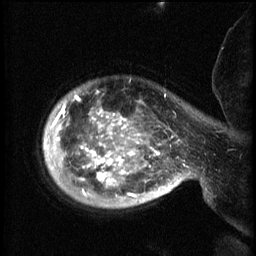
Breast MRI (dynamic contrast-enhanced), one sagittal slice. Position 51 of 60 along the scan axis. 3 images stored at this slice position (order not interpretable as contrast timing). 1.5 T. TE 4.2 ms, TR 8.2 ms. 2.3 mm slice thickness. 256 × 256 image matrix. Patient: female, 50 years.
Outlined on this slice (semi-automatically segmented with operator editing):
- analysis volume of interest (the breast-tissue region the enhancement analysis was run in; not a lesion): bounding box (x1, y1, x2, y2) in pixels: (50, 84, 169, 209)
- tumour enhancement mask (voxels above the 70 % enhancement threshold inside the analysis volume of interest): (52, 96, 167, 197)